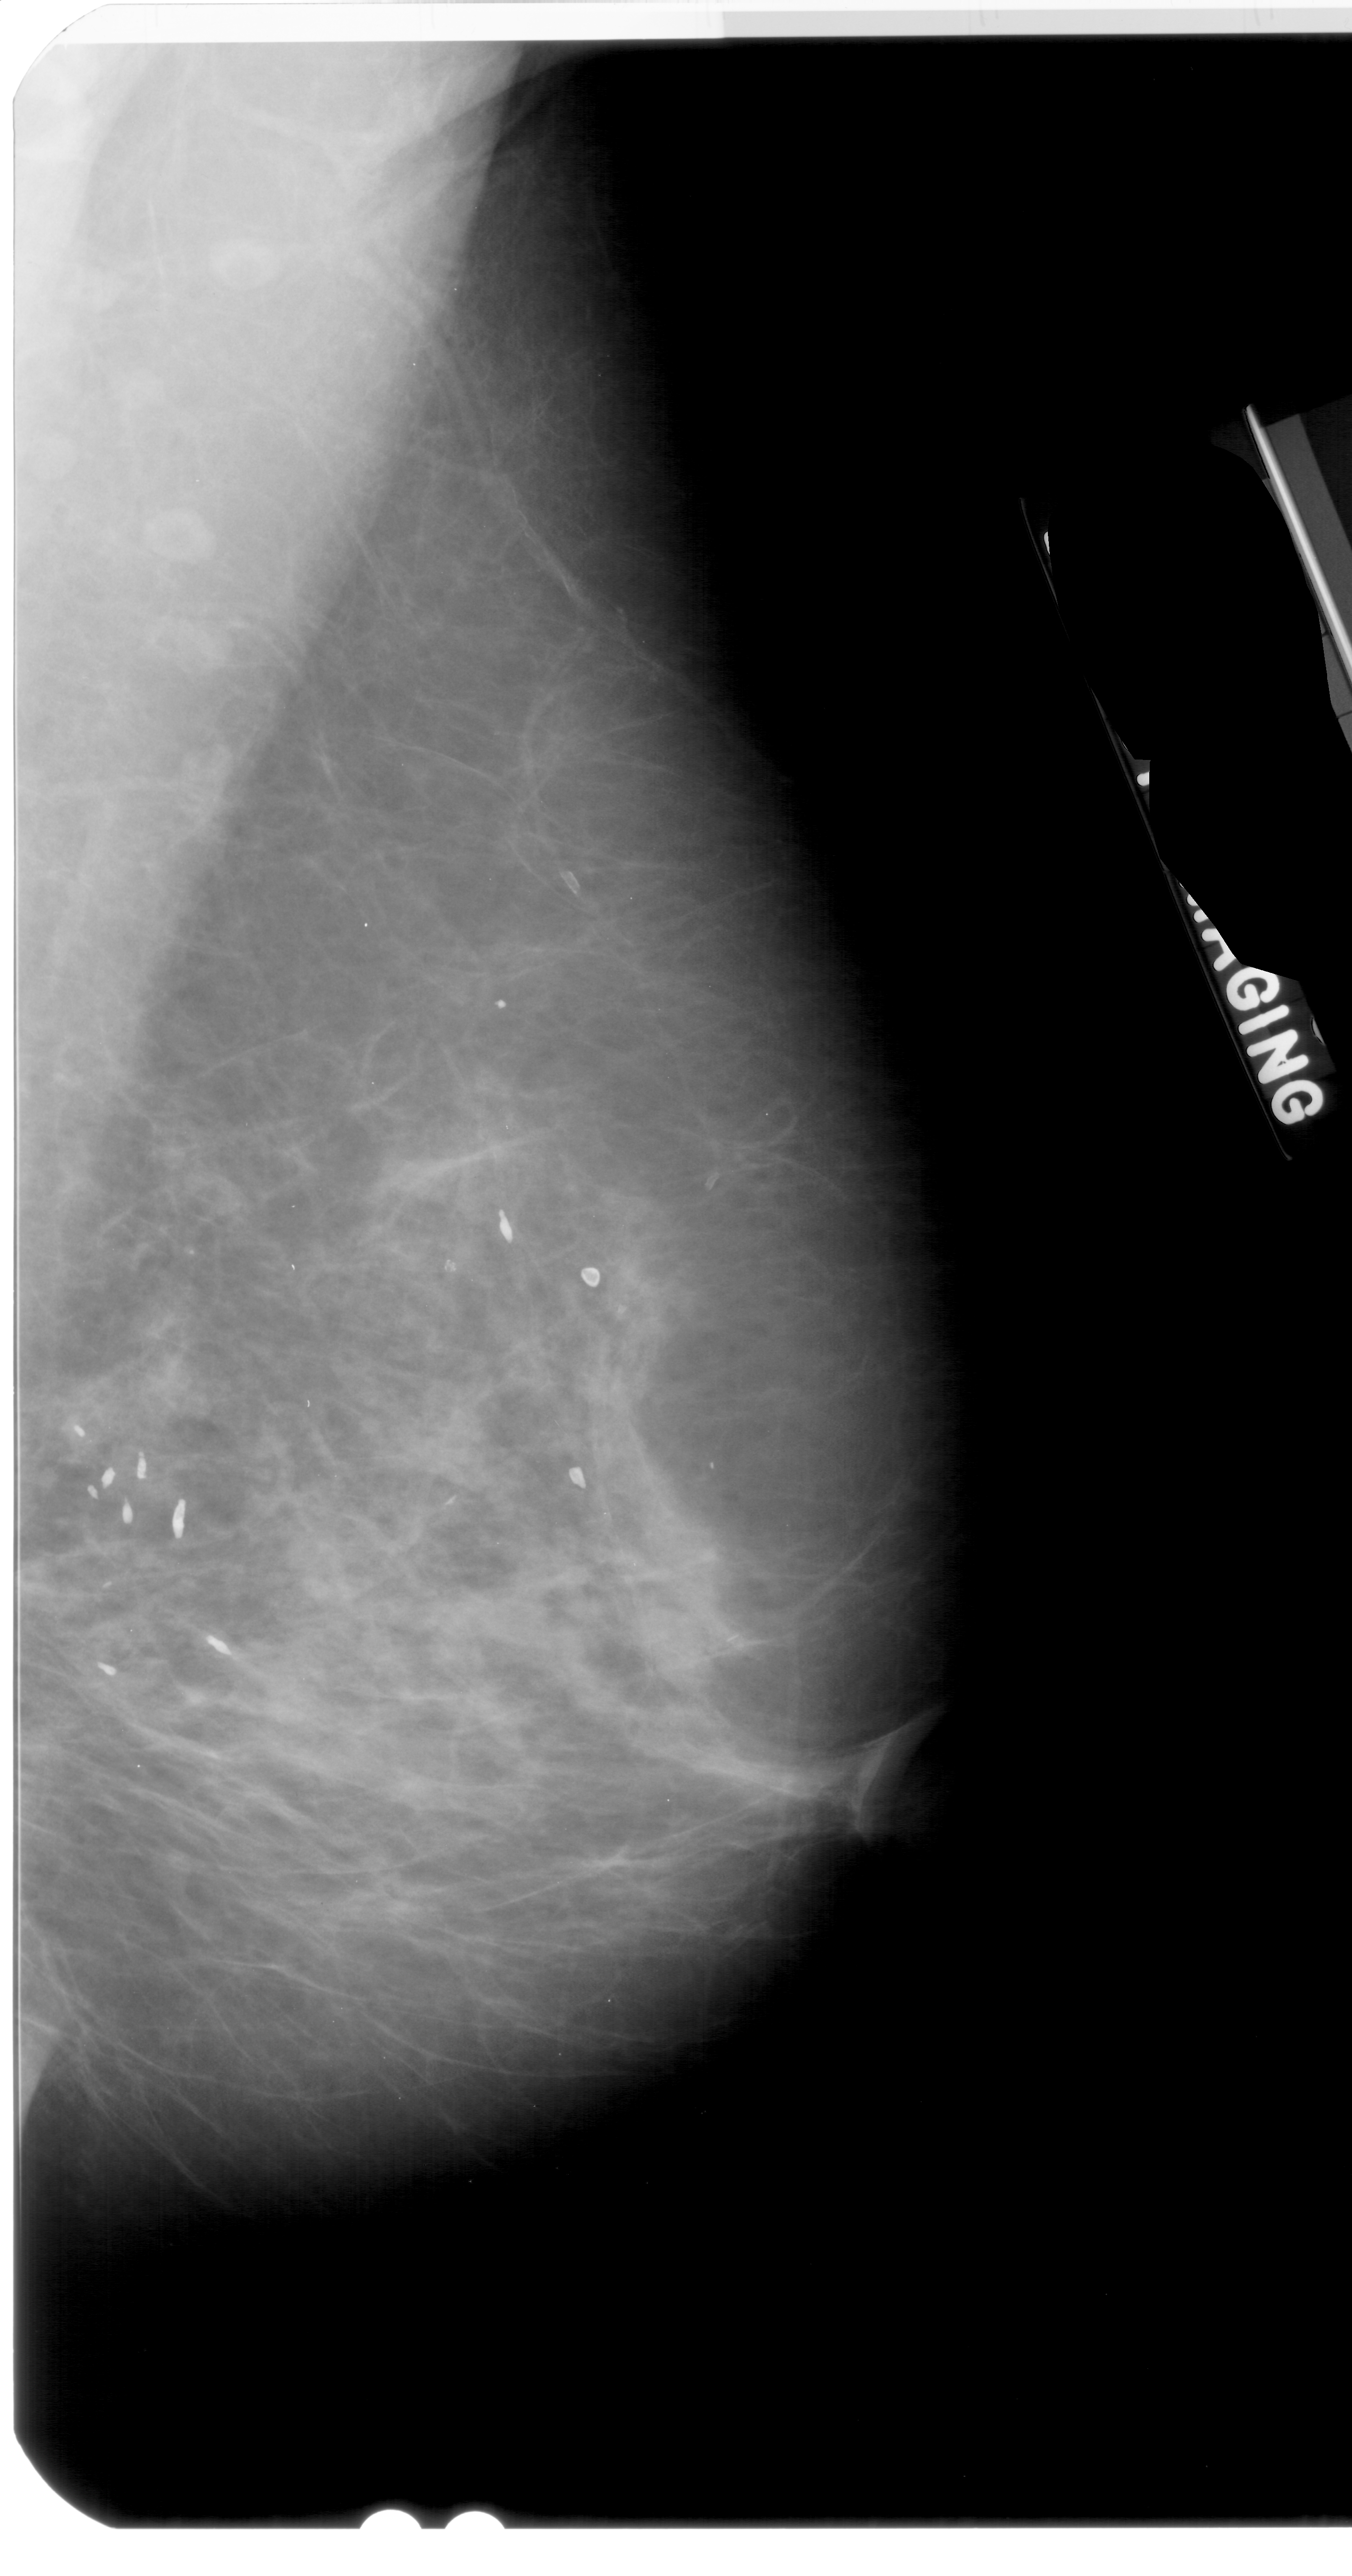
Digitized screen-film mammogram. Right breast. MLO view. BI-RADS breast density category 2 (scale 1–4). 1352 × 2576 image matrix.
Expert-marked regions of interest on this film, with their recorded descriptors:
- mass, shape lobulated, margins ill defined; BI-RADS assessment category 4; pathology (as recorded): benign: bounding box (x1, y1, x2, y2) in pixels: (618, 1608, 712, 1691)